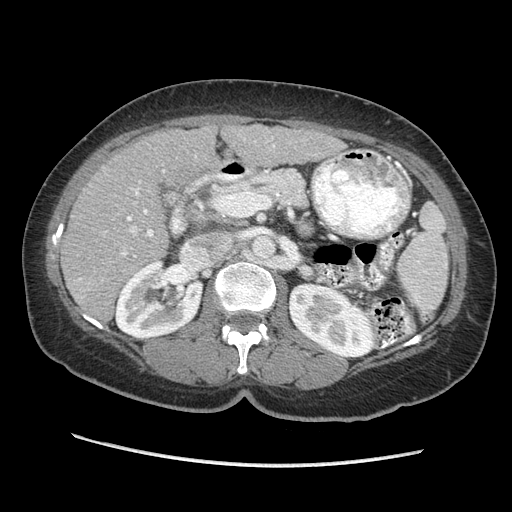
Contrast-enhanced abdominal CT (liver protocol), one axial slice; slice 119 of 170 in the series (ordered by position); reconstruction kernel STANDARD; soft-tissue window (W 400 / L 40 HU); 2.5 mm slice thickness; 512 × 512 image matrix, field of view 360 × 360 mm. From the clinical record (not read from this slice): diagnosis: hepatocellular carcinoma (patient treated with transarterial chemoembolisation; whether this scan precedes or follows treatment is not stated here); TNM stage (as recorded): Stage-II; Child-Pugh class: A; tumour differentiation: no biopsy; tumour nodularity: multinodular.
Outlined on this slice (semi-automatically segmented with operator editing):
- liver parenchyma outside the tumour (the mass and vessels are separate outlines, so this box may not span the whole liver): bounding box <62,123,345,320> (left, top, right, bottom; pixels)
- liver vessels: <122,145,275,257>